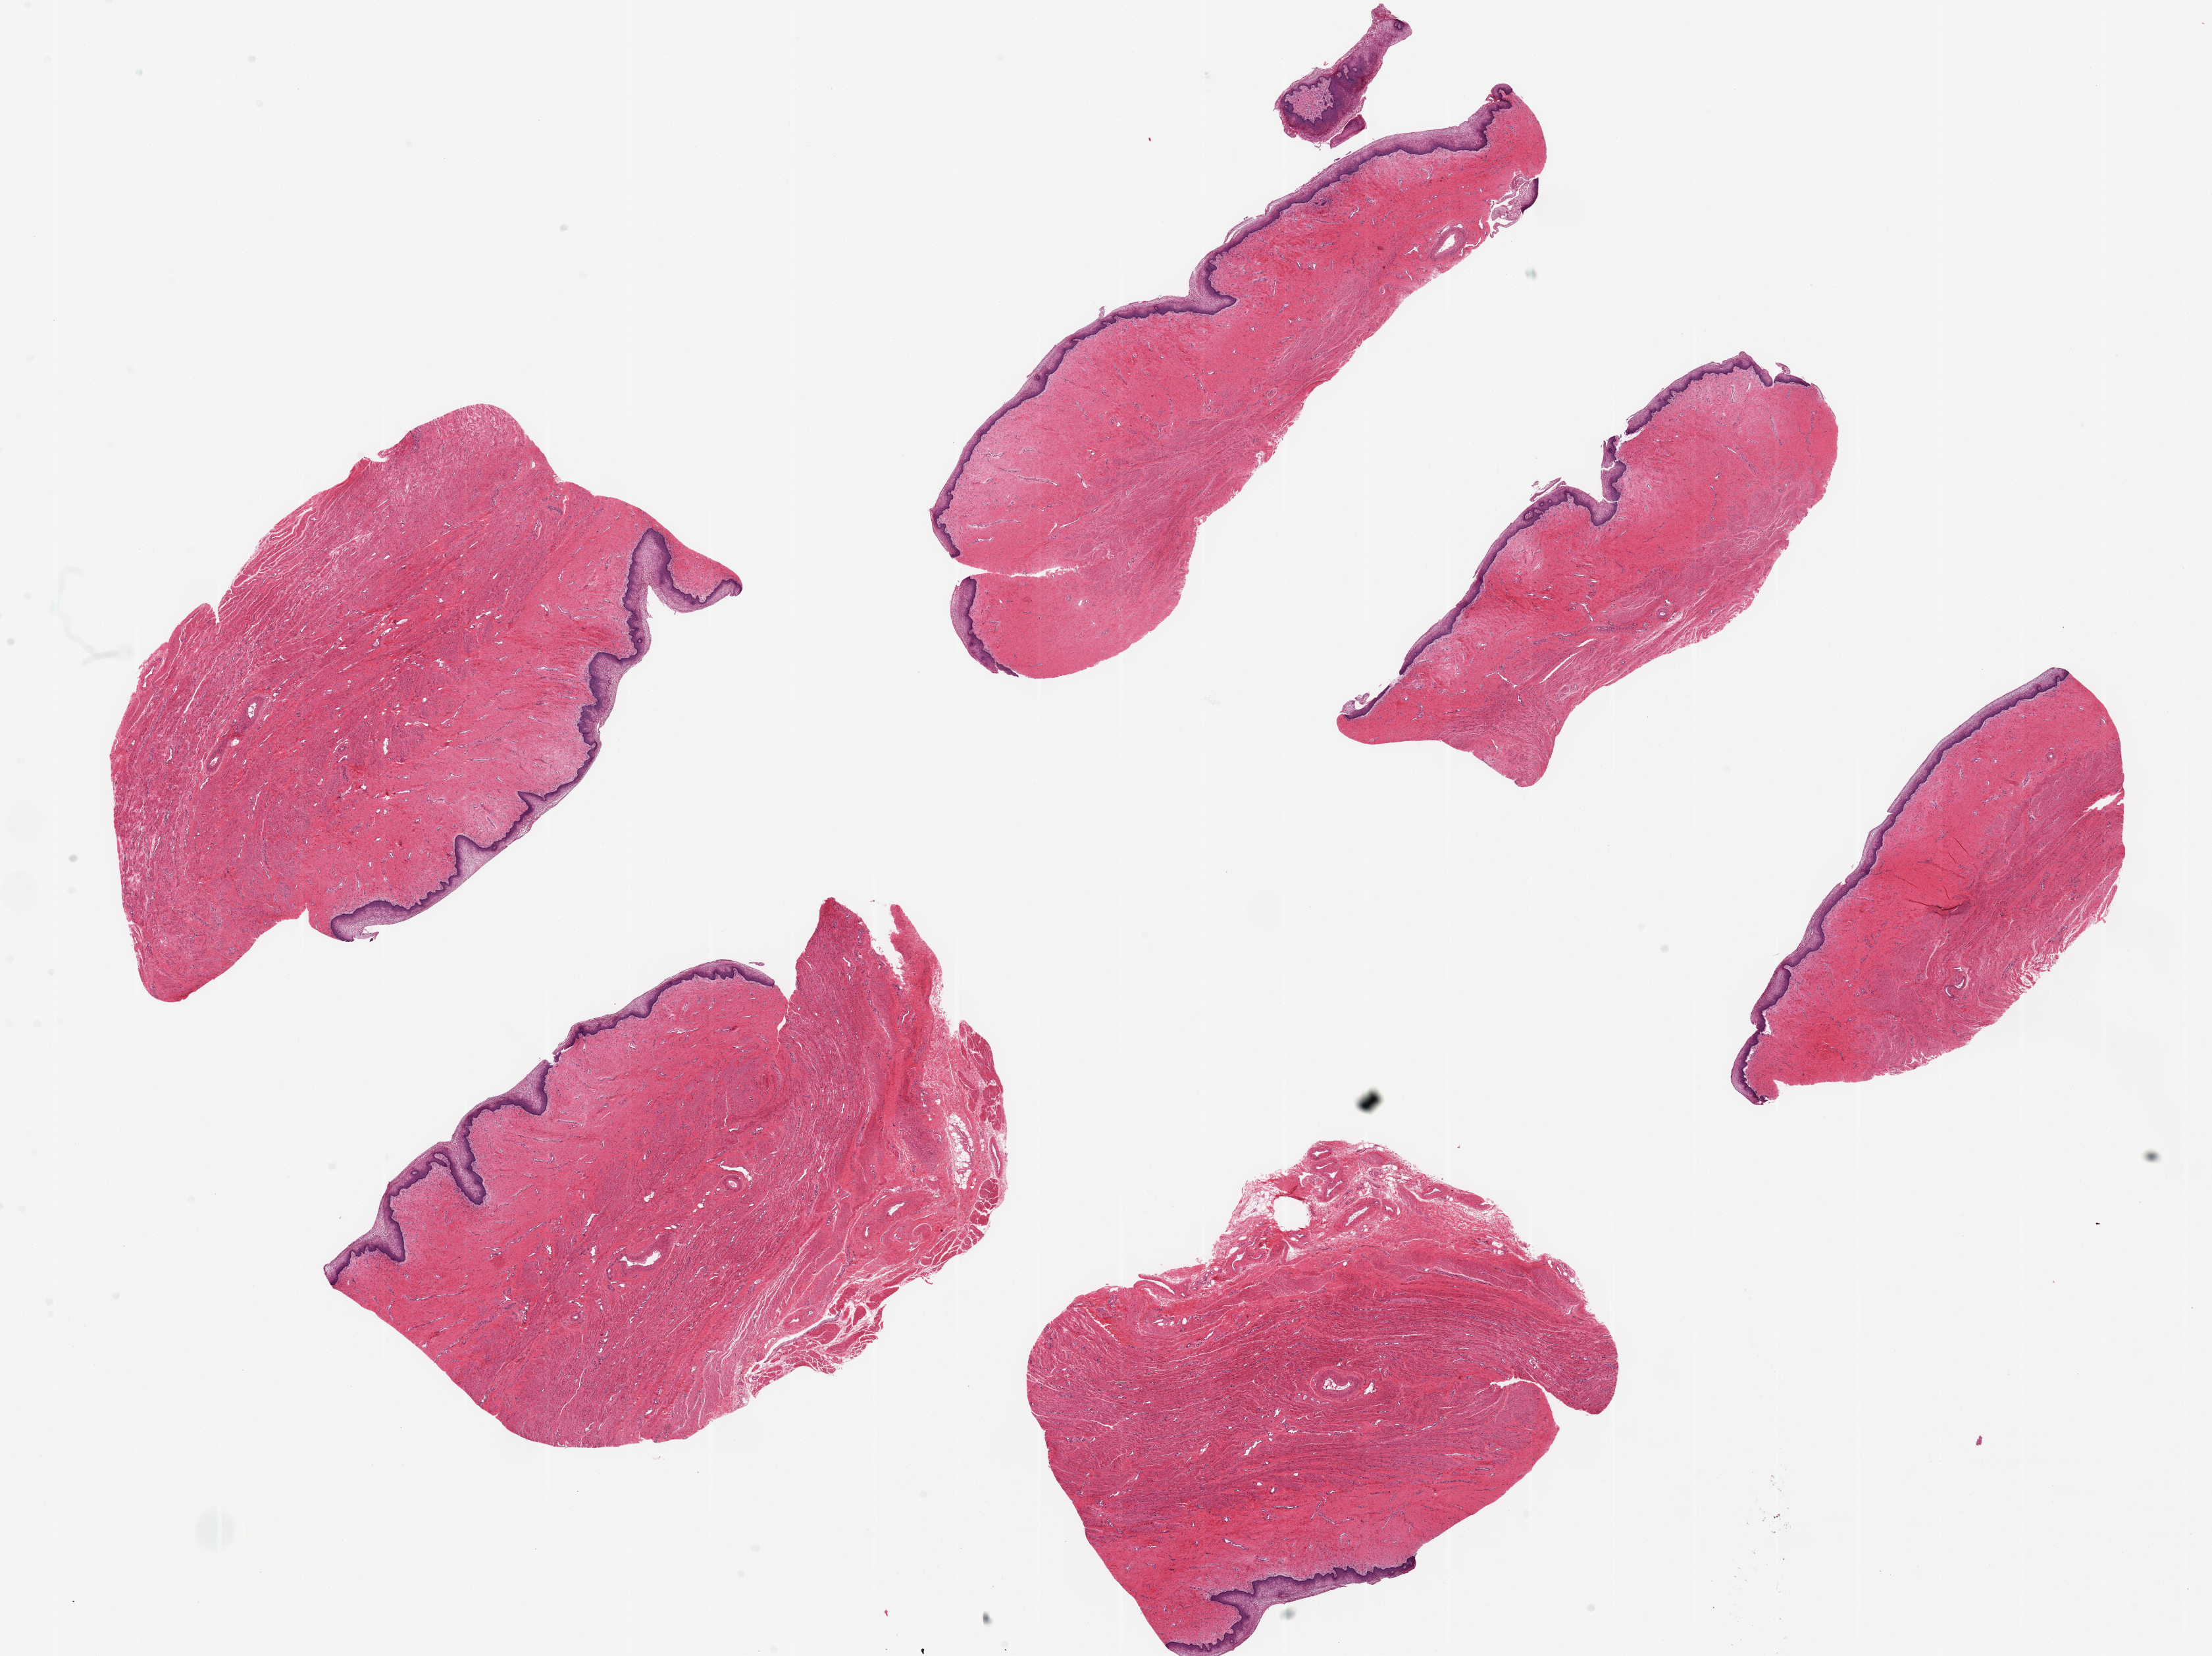
Hematoxylin and eosin (H&E) whole-slide image — a low-resolution overview of the entire scanned area, about 26.6 x 19.9 mm; PAXgene-fixed paraffin-embedded (PFPE) section; section of vagina (target tissue); tissue donor sample. Donor: female.
- pathologist's review note for this sample: 6 pieces, ~9x3mm, 5x6mm; all with squamous lining